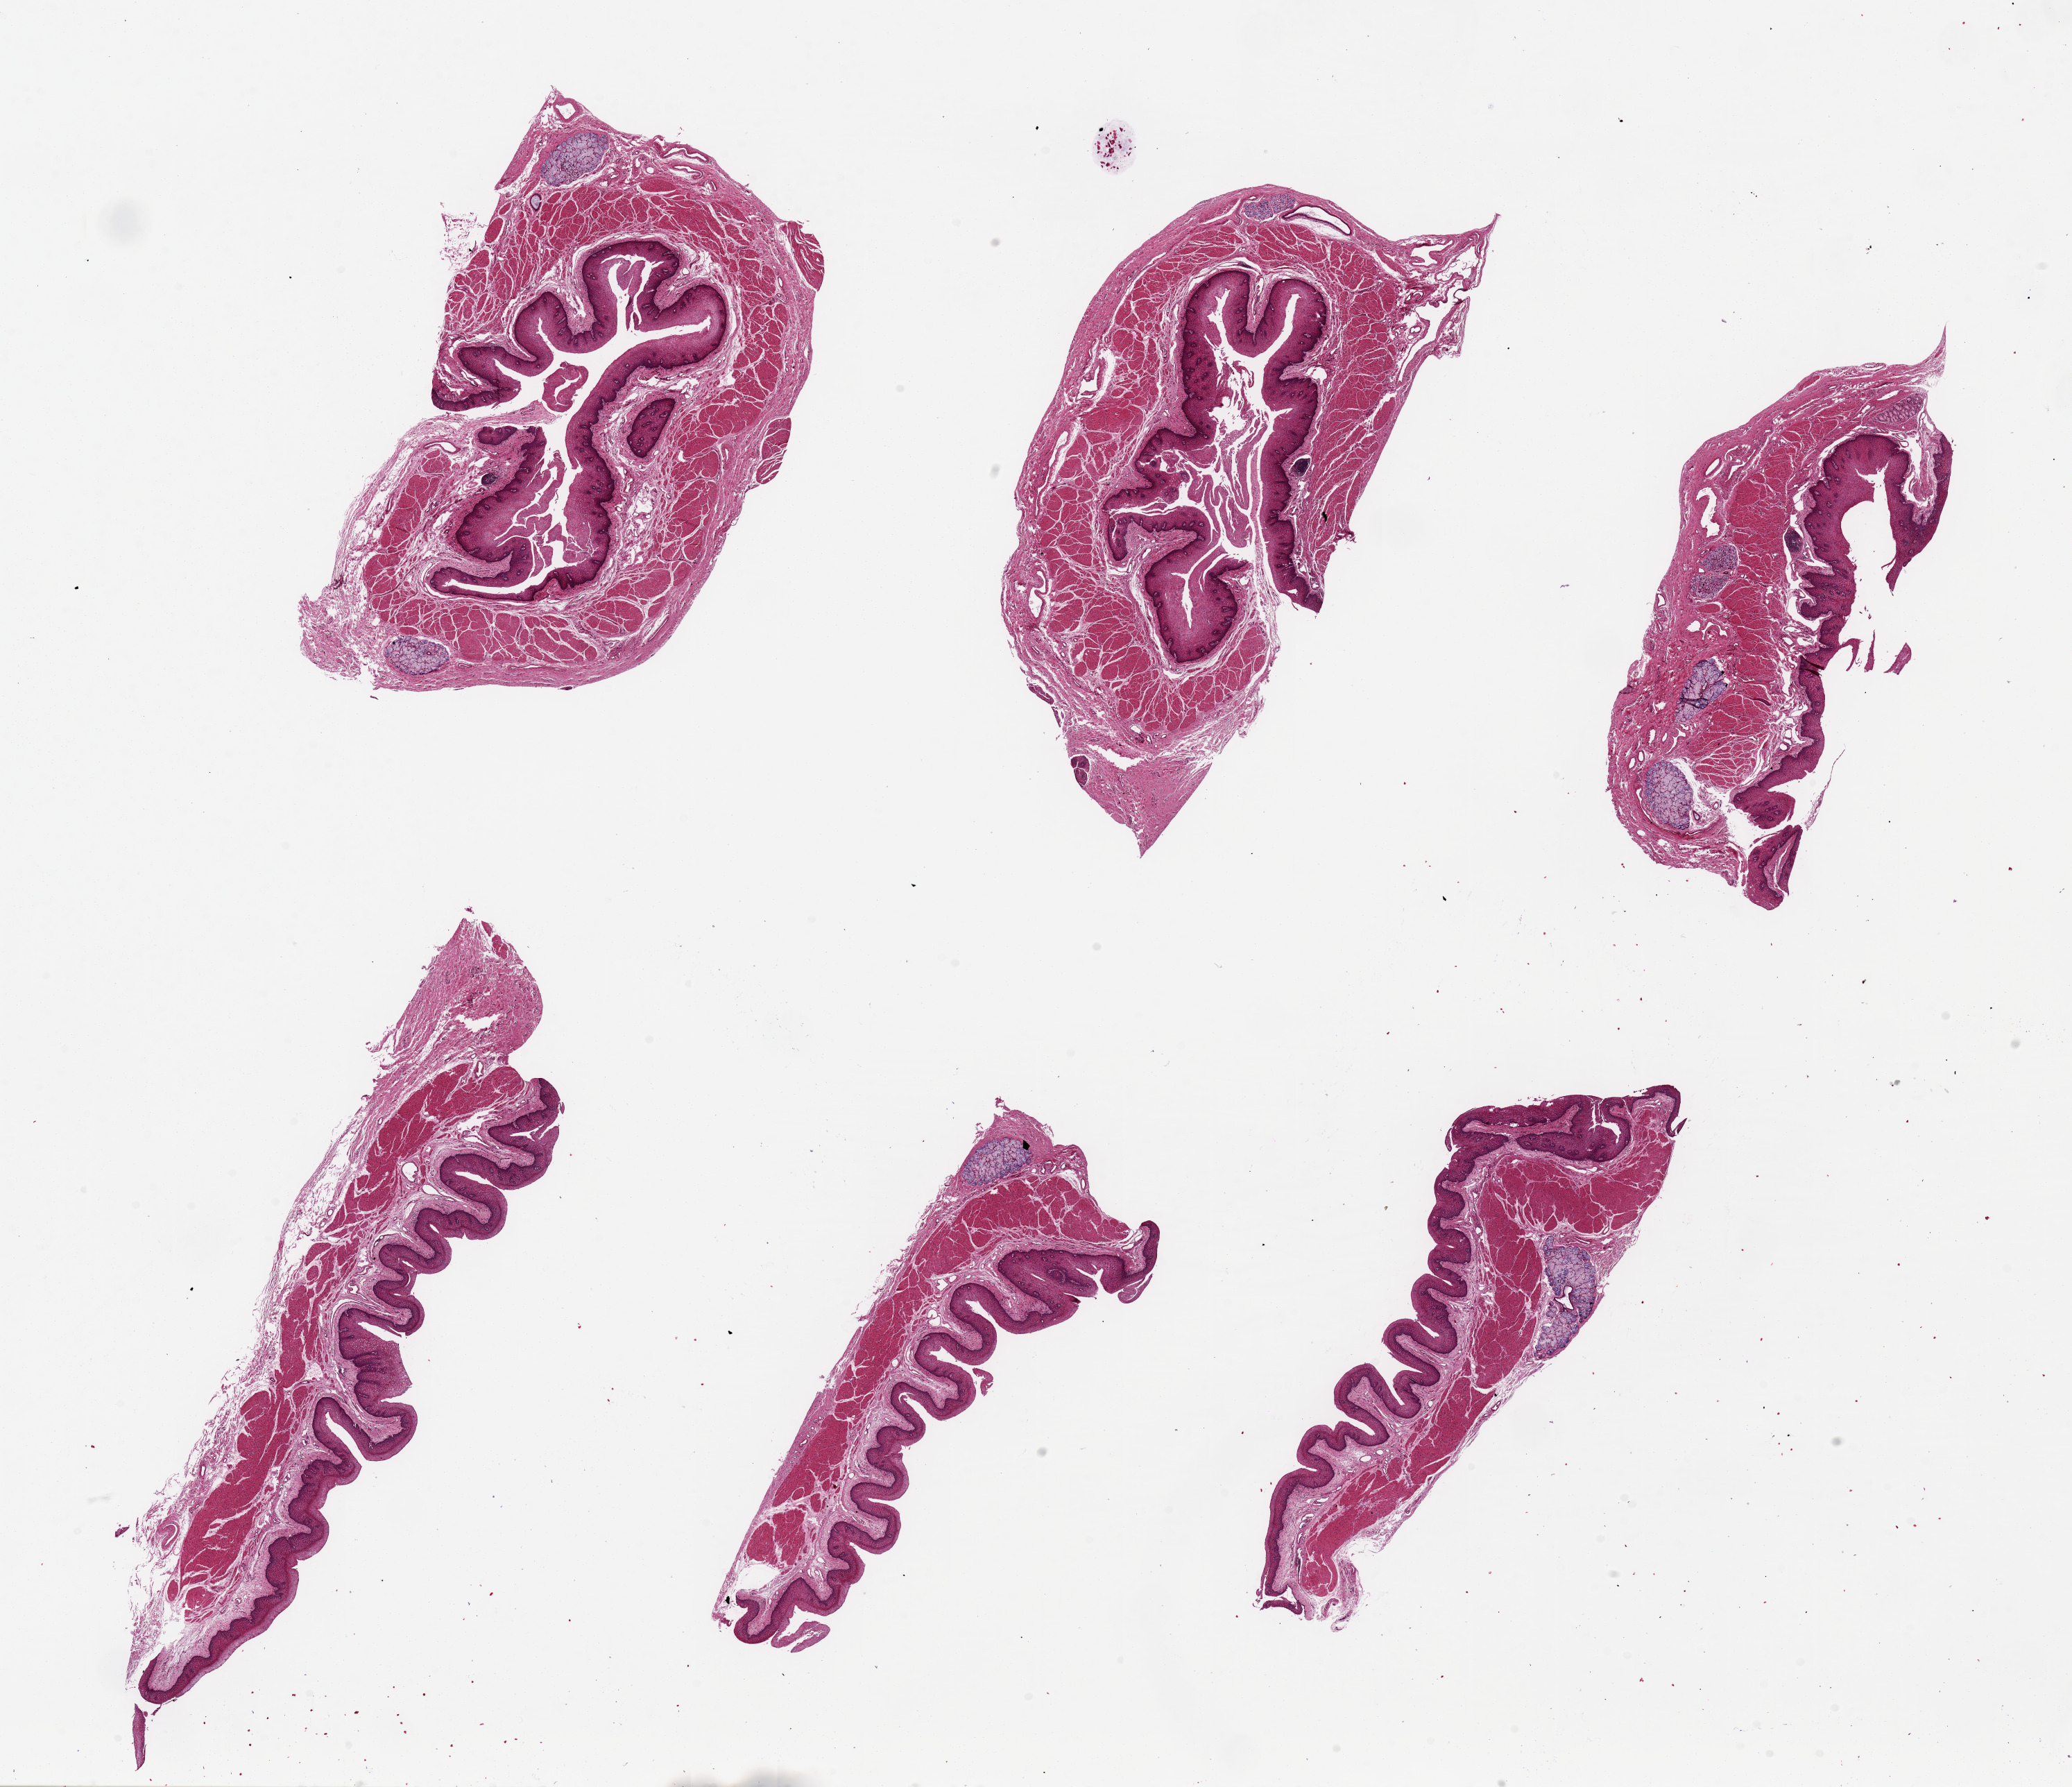
H&E whole-slide image, a low-resolution overview of the entire scanned area, about 23.6 x 20.4 mm. PAXgene-fixed, paraffin-embedded tissue. Section of esophageal mucous membrane (target tissue). Tissue donor sample.
* review note (as recorded): 6 pieces ~7x2mm, squamous mucosa well-preserved, up to 10% thickness